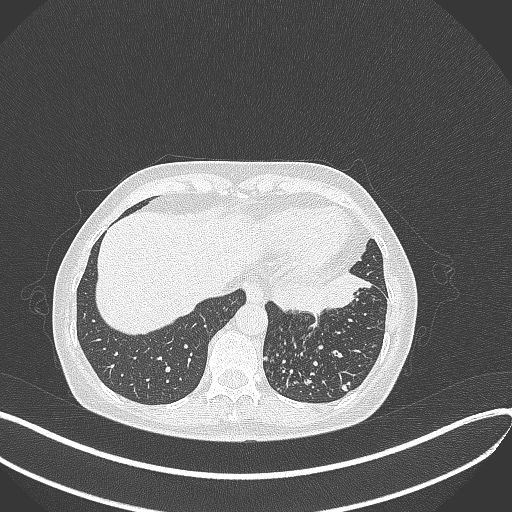
Chest CT, one axial slice. Position 93 of 429 along the scan axis. Reconstruction kernel B70f. 100 kVp. Lung window (W 1500 / L -600 HU). 1 mm slice thickness. 512 × 512 image matrix, field of view 400 × 400 mm. Patient: female, 63 years. Case-level facts recorded for this patient, not image findings: clinical TNM (as recorded): T1b N0 M0; histopathological grade: G2-3.
Outlined on this slice (rectangle marked by the reading radiologist):
- lung tumour (recorded histology: adenocarcinoma): bounding box (x1, y1, x2, y2) in pixels: (275, 274, 372, 314)